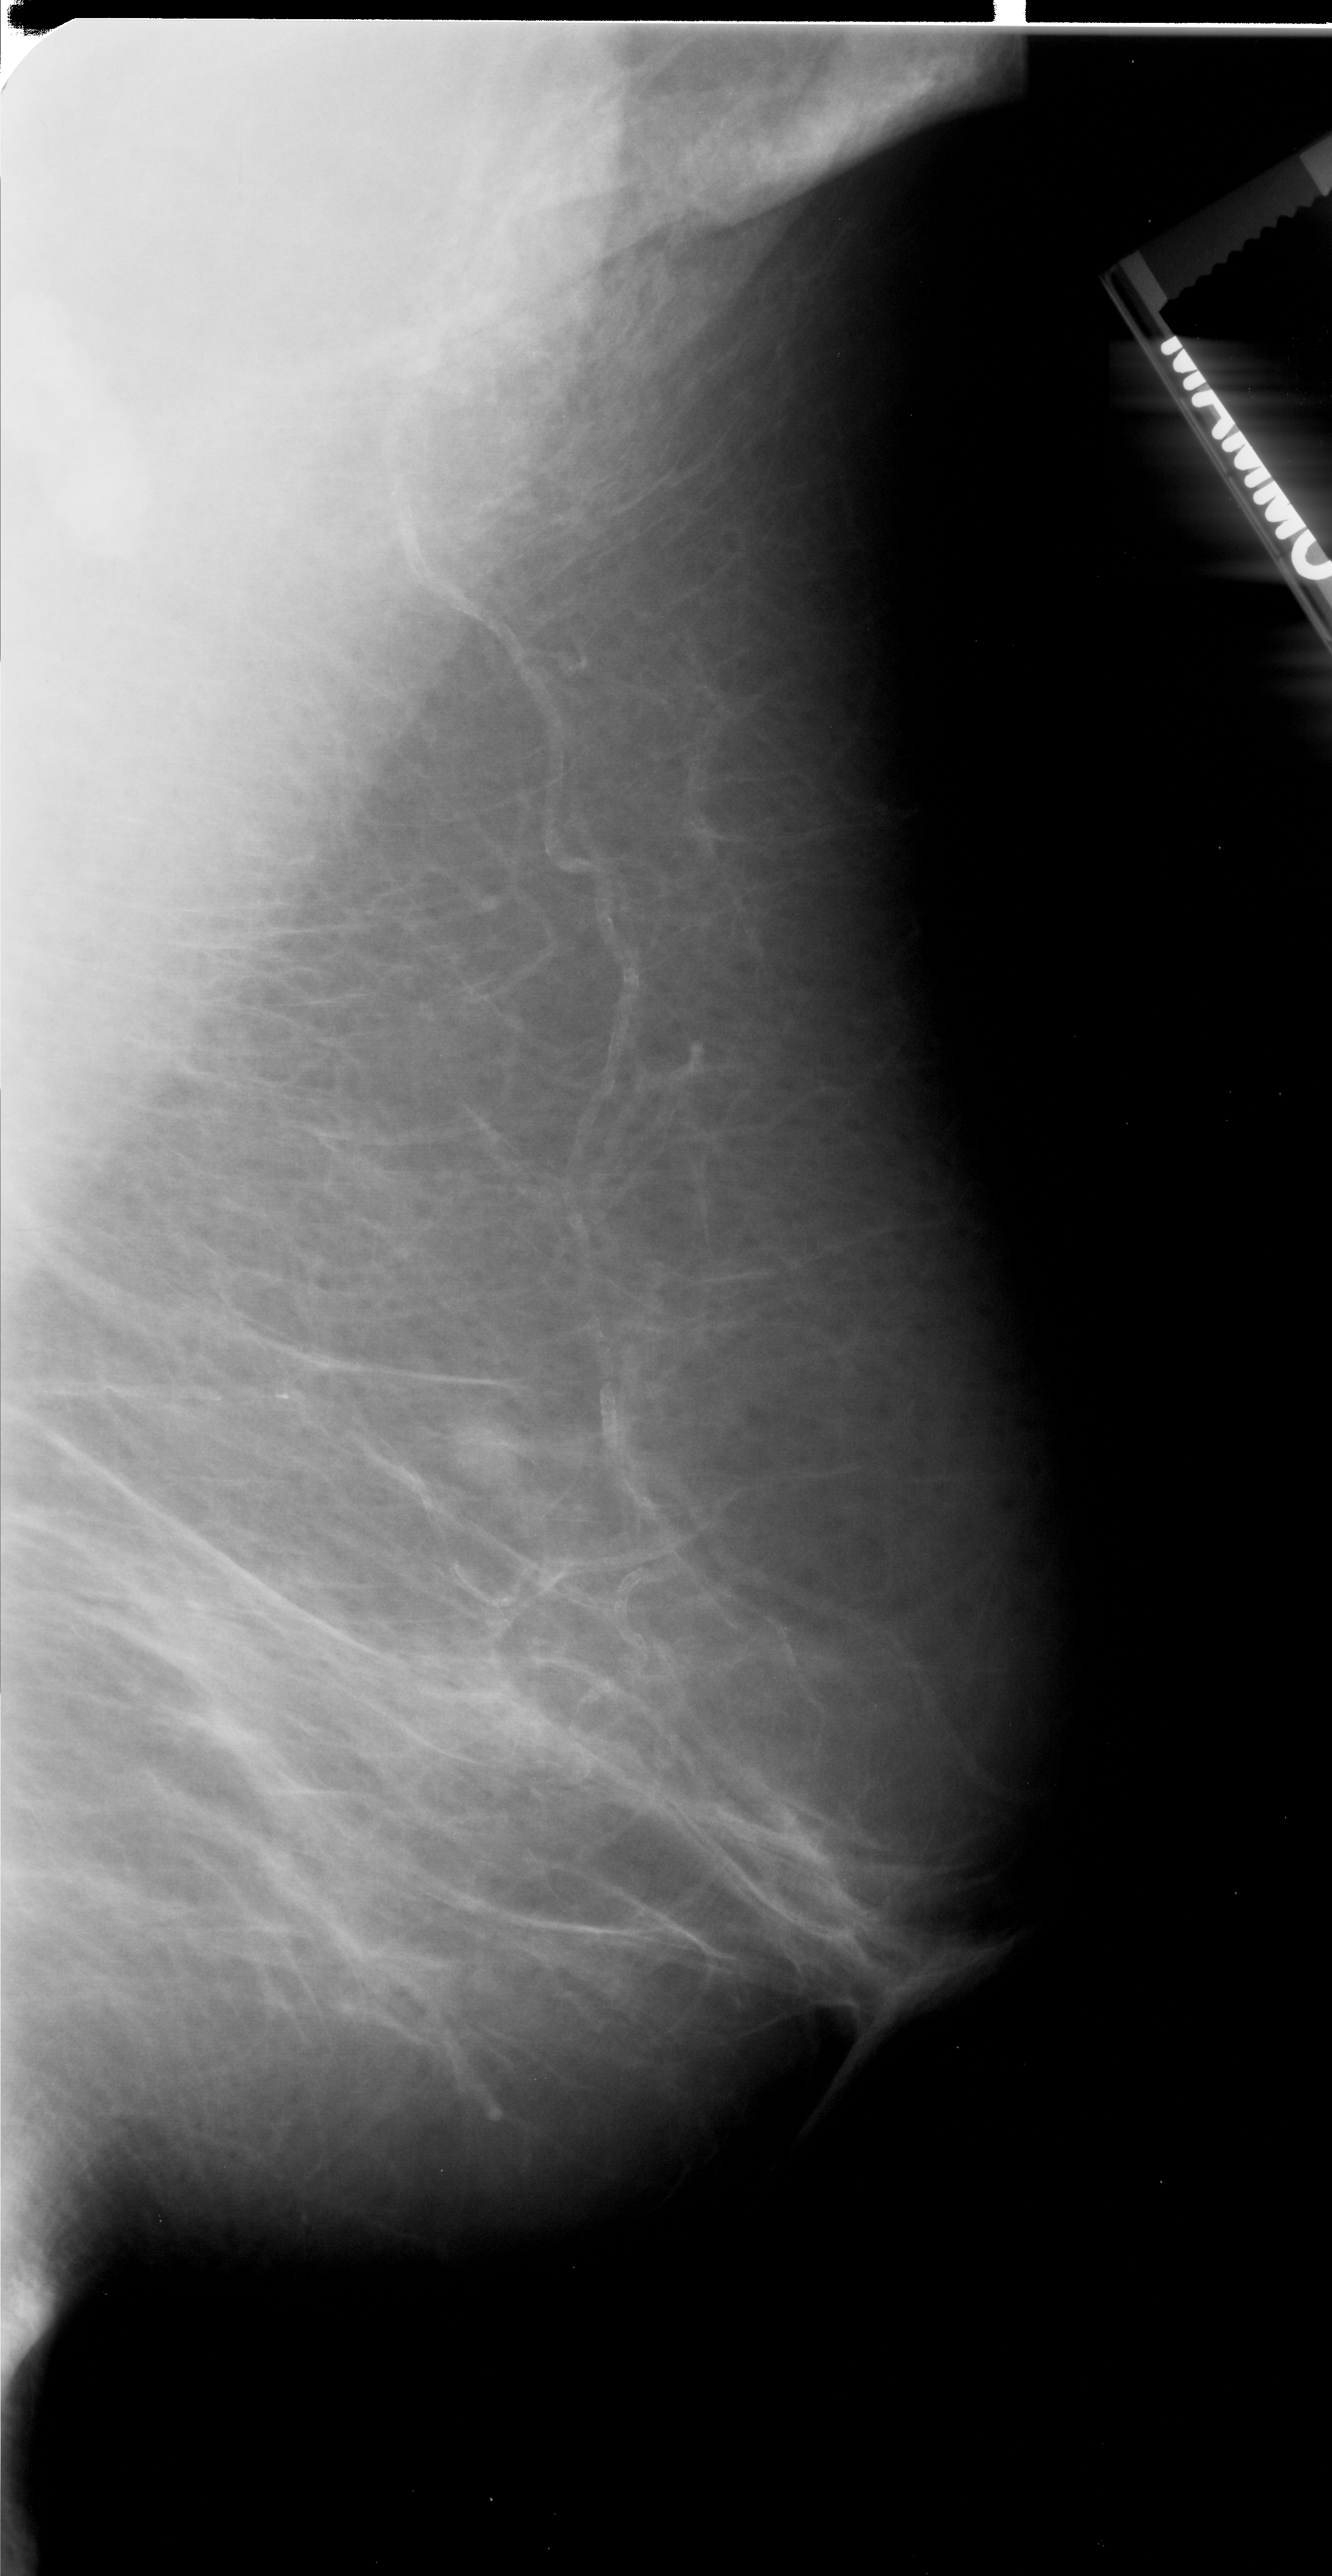
Digitized screen-film mammogram, right breast, MLO view, BI-RADS breast density category 1 (scale 1–4).
Marked abnormality: mass, shape irregular, margins ill defined; BI-RADS assessment category 4; pathology (as recorded): malignant.